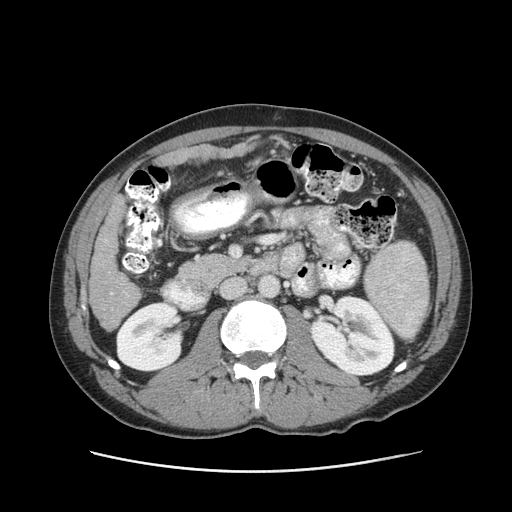
Contrast-enhanced abdominal CT (liver protocol), one axial slice. Reconstruction kernel STANDARD. Soft-tissue window (W 400 / L 40 HU). 512 × 512 image matrix, field of view 380 × 380 mm. Case-level facts recorded for this patient, not image findings: diagnosis: hepatocellular carcinoma (patient treated with transarterial chemoembolisation; whether this scan precedes or follows treatment is not stated here); TNM stage (as recorded): Stage-II; Child-Pugh class: A; tumour differentiation: moderately differentiated; tumour size: 1 cm.
Outlined on this slice (semi-automatic segmentation, software-assisted and operator-edited):
- liver parenchyma outside the tumour (the mass and vessels are separate outlines, so this box may not span the whole liver): box from (x=90, y=196) to (x=140, y=330) px
- liver vessels: (x=105, y=241)–(x=113, y=295)